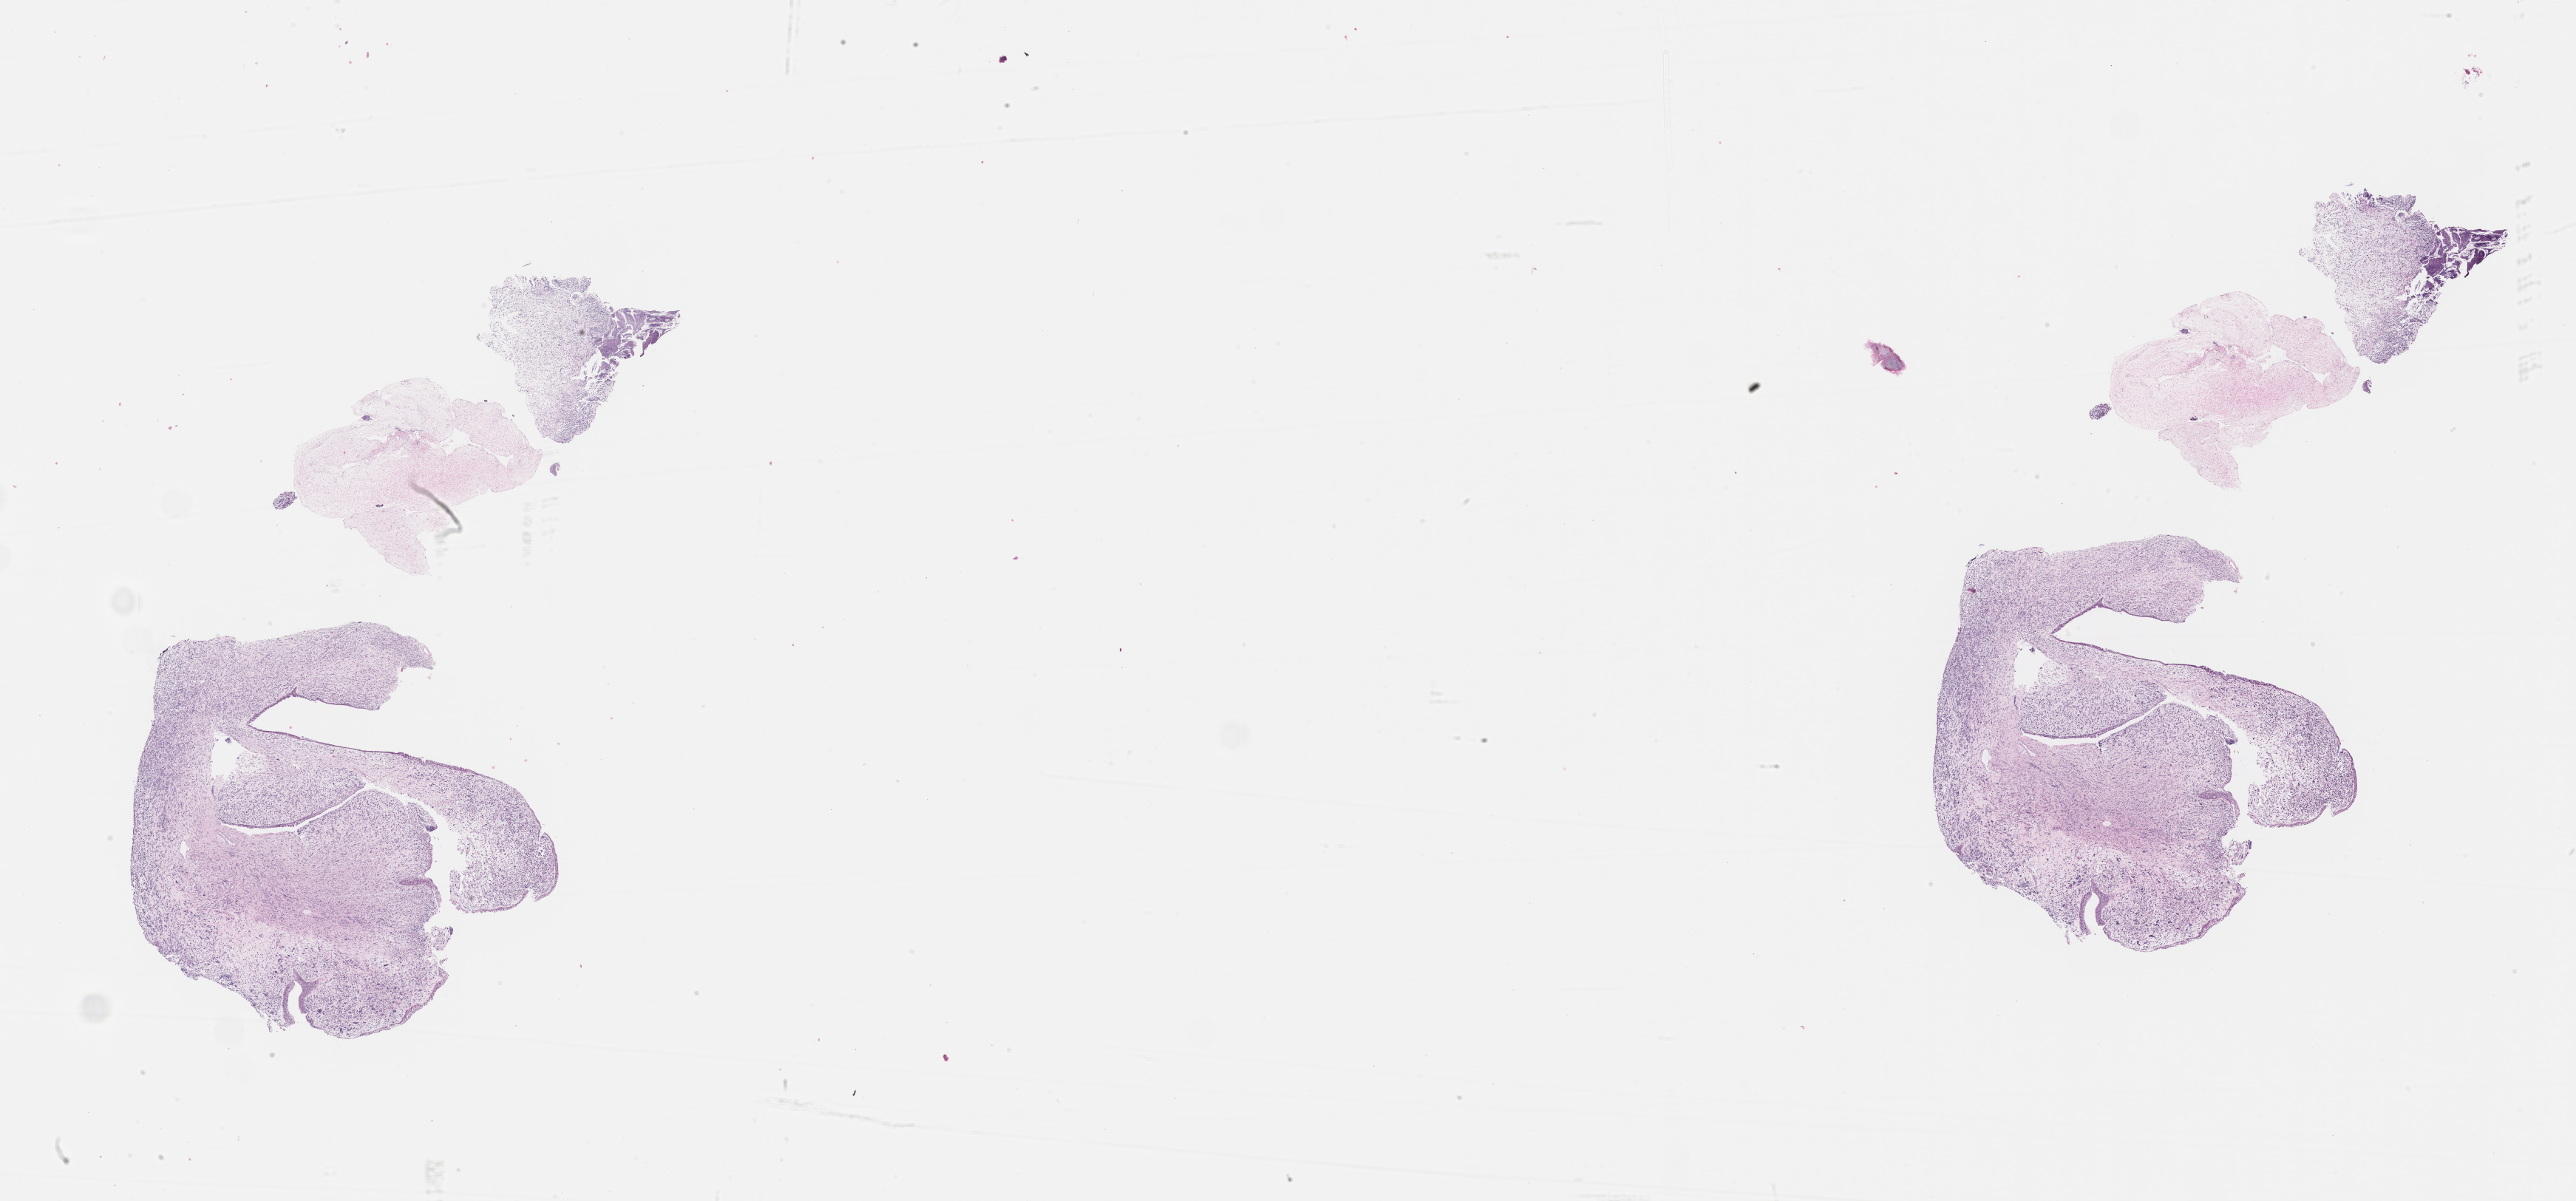
Haematoxylin and eosin whole-slide image of tumor tissue — whole scanned area (about 28.2 x 13.1 mm) shown as a low-resolution overview, formalin-fixed paraffin-embedded section. Patient: male, age 1.1 years at diagnosis.
Diagnosis: rhabdomyosarcoma; histological classification: botryoid. Stage (as recorded): 3. Metastatic status at presentation (as recorded): non-metastatic.